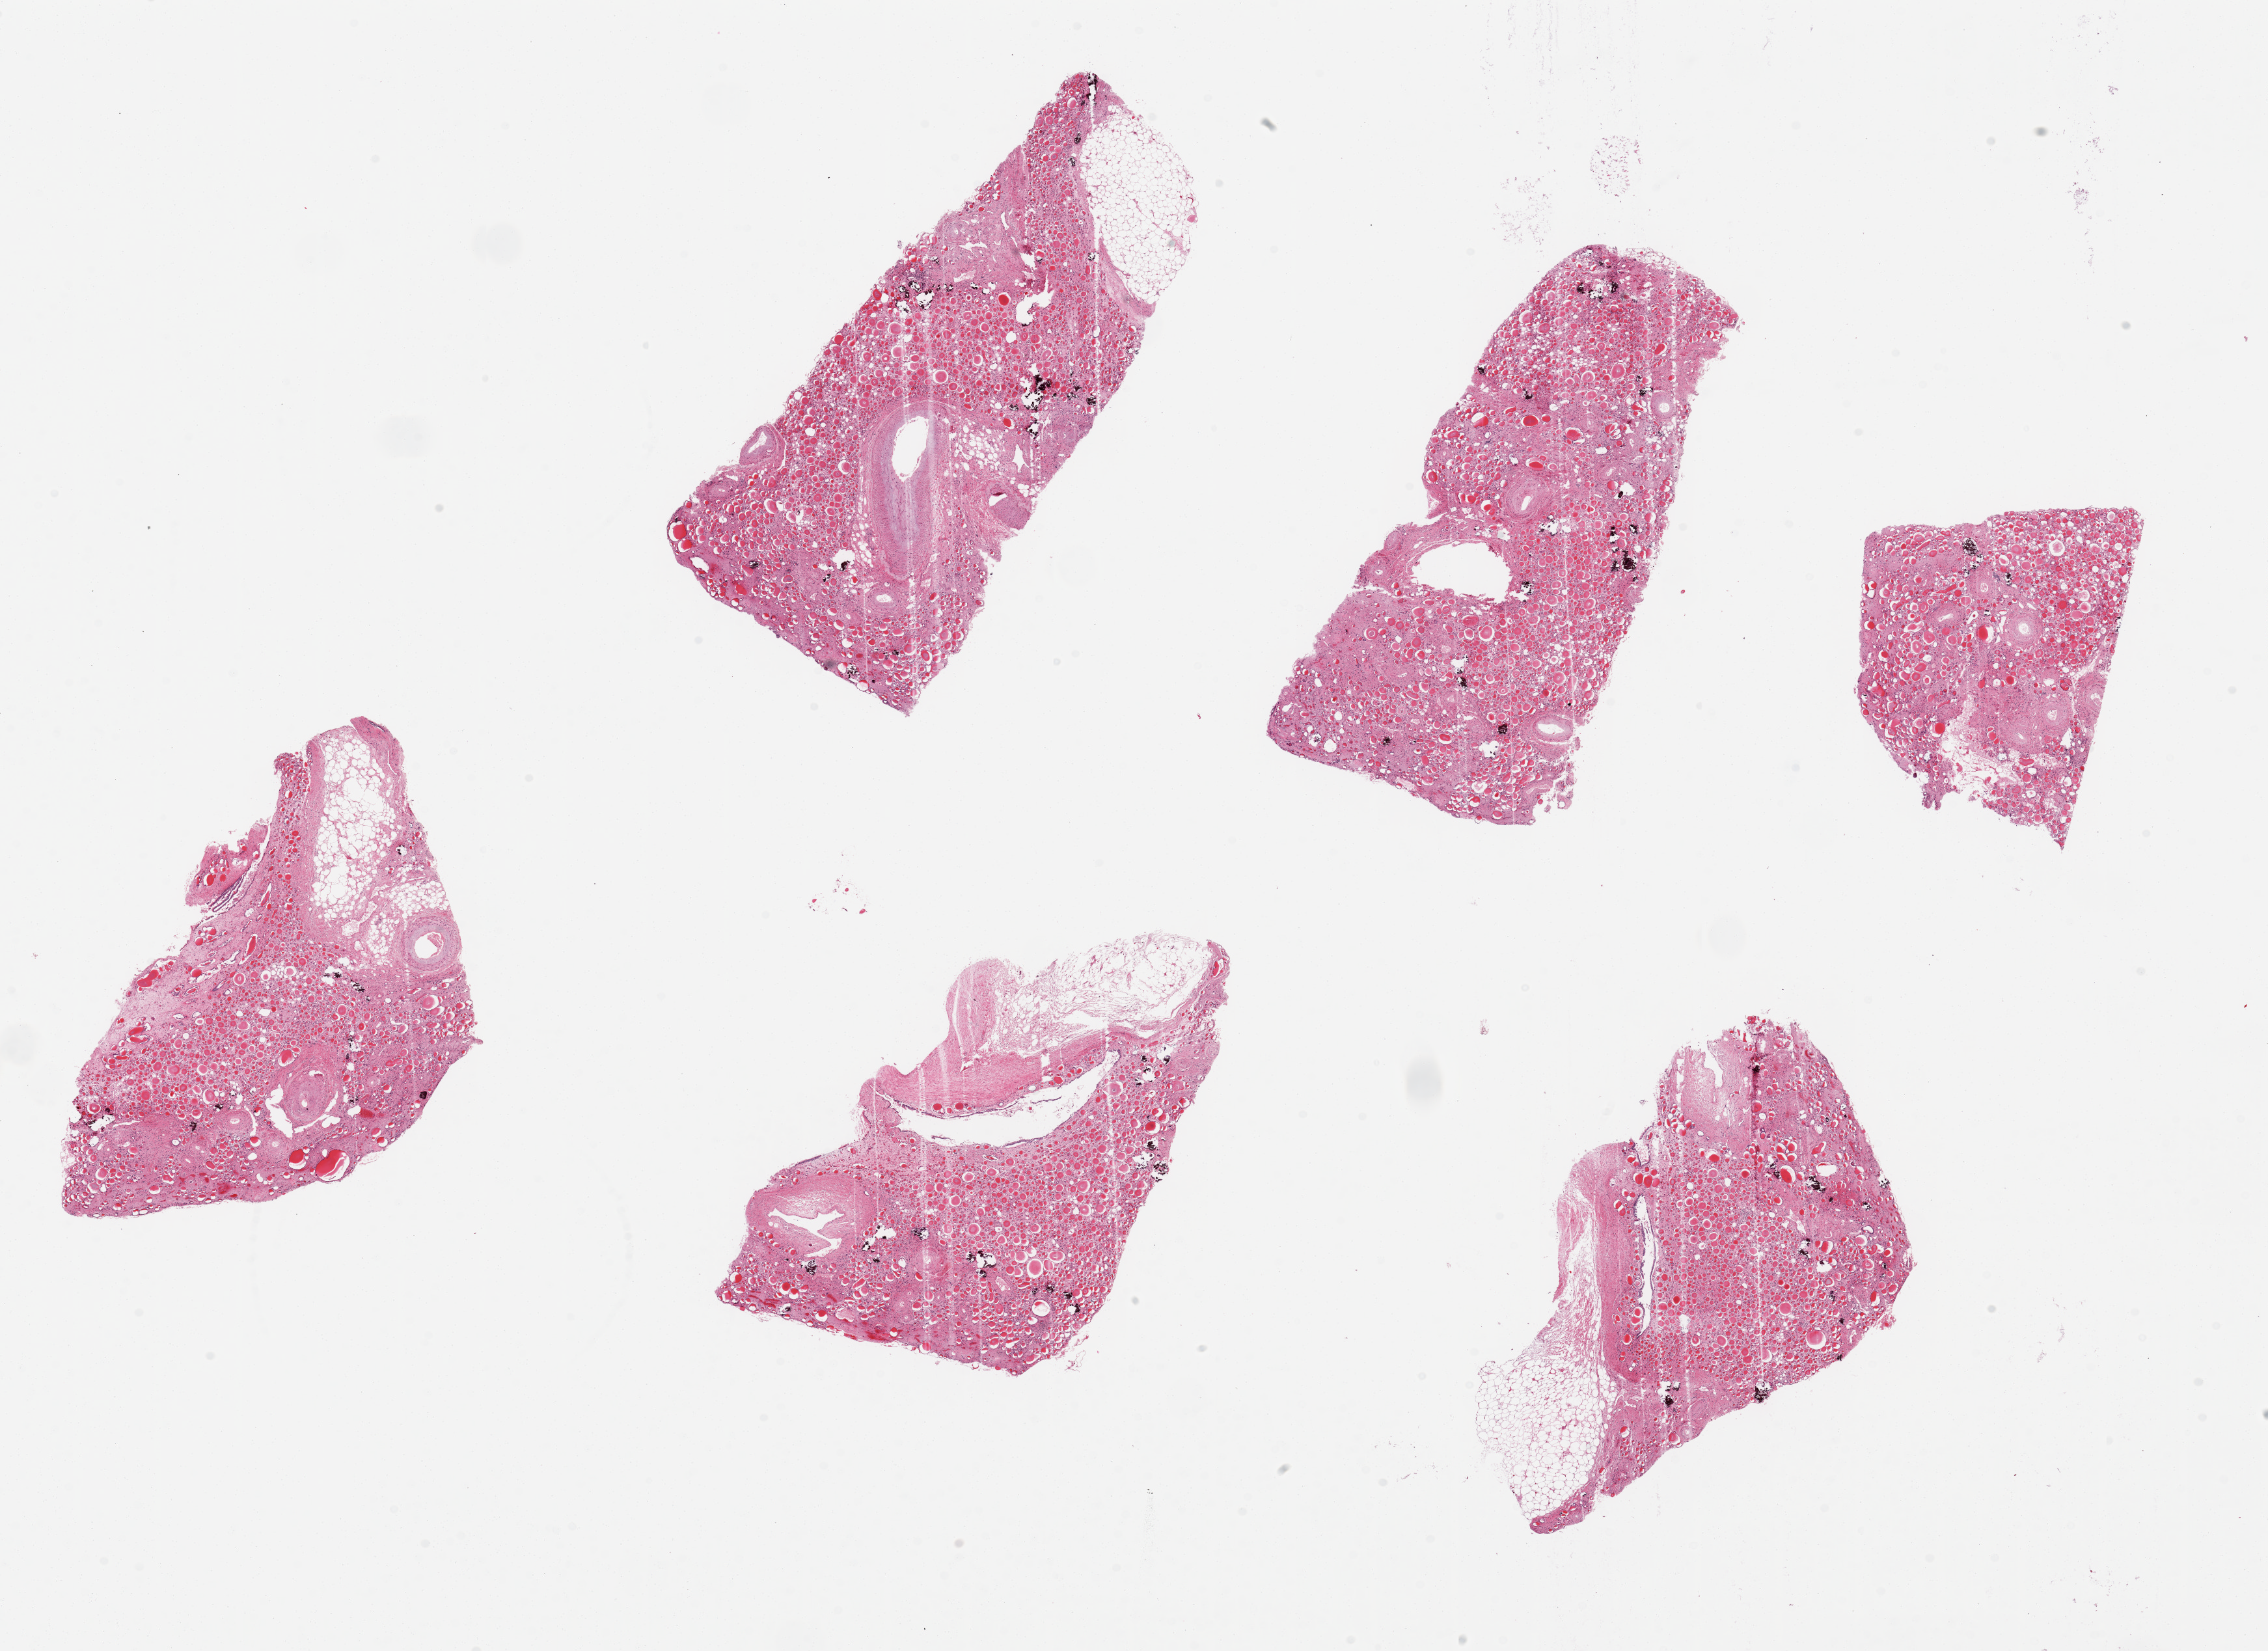
Whole-slide image, H&E stain — low-resolution overview of the scanned area, about 27.6 x 20.1 mm (acquisition: 20x scan), PAXgene-fixed paraffin-embedded (PFPE) section, section of renal cortex (target tissue), donor tissue sample. Donor: female.
Review note (as recorded): 6 pieces measuring up to 7.5x3.6 mm; all show extensive destruction of renal parenchyma with fibrosis, calcification and ???thyroidization??? characteristic of chronic pyelonephritis; arteries greatly thickened; no viable glomeruli.